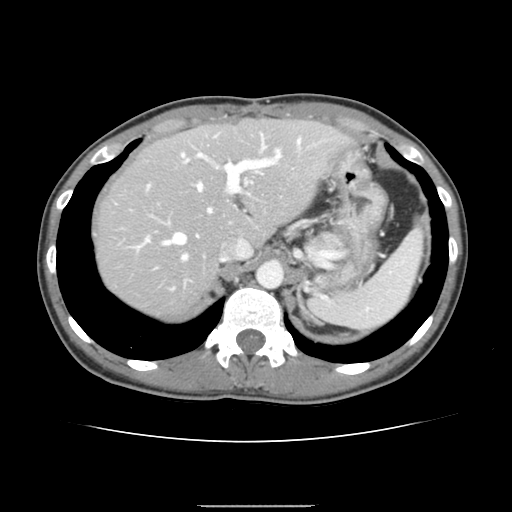
Contrast-enhanced abdominal CT, one axial slice. Position 110 of 150 along the scan axis. 120 kVp. Intravenous contrast given. Soft-tissue window (W 400 / L 40 HU). 512 × 512 image matrix. Female patient, age 32 years. From the clinical record (not read from this slice): diagnosis: colorectal cancer liver metastases, imaged before liver resection; multiple liver metastases: yes; largest metastasis: 0.7 cm; chemotherapy before resection: yes.
Outlined on this slice (outlined manually by an expert reader):
- hepatic veins: bounding box [x1, y1, x2, y2] px = [155, 150, 281, 269]
- liver: [97, 121, 346, 317]
- planned liver remnant (the part of the liver to remain after resection): [97, 120, 347, 276]
- portal vein (with intrahepatic branches): [135, 134, 301, 250]